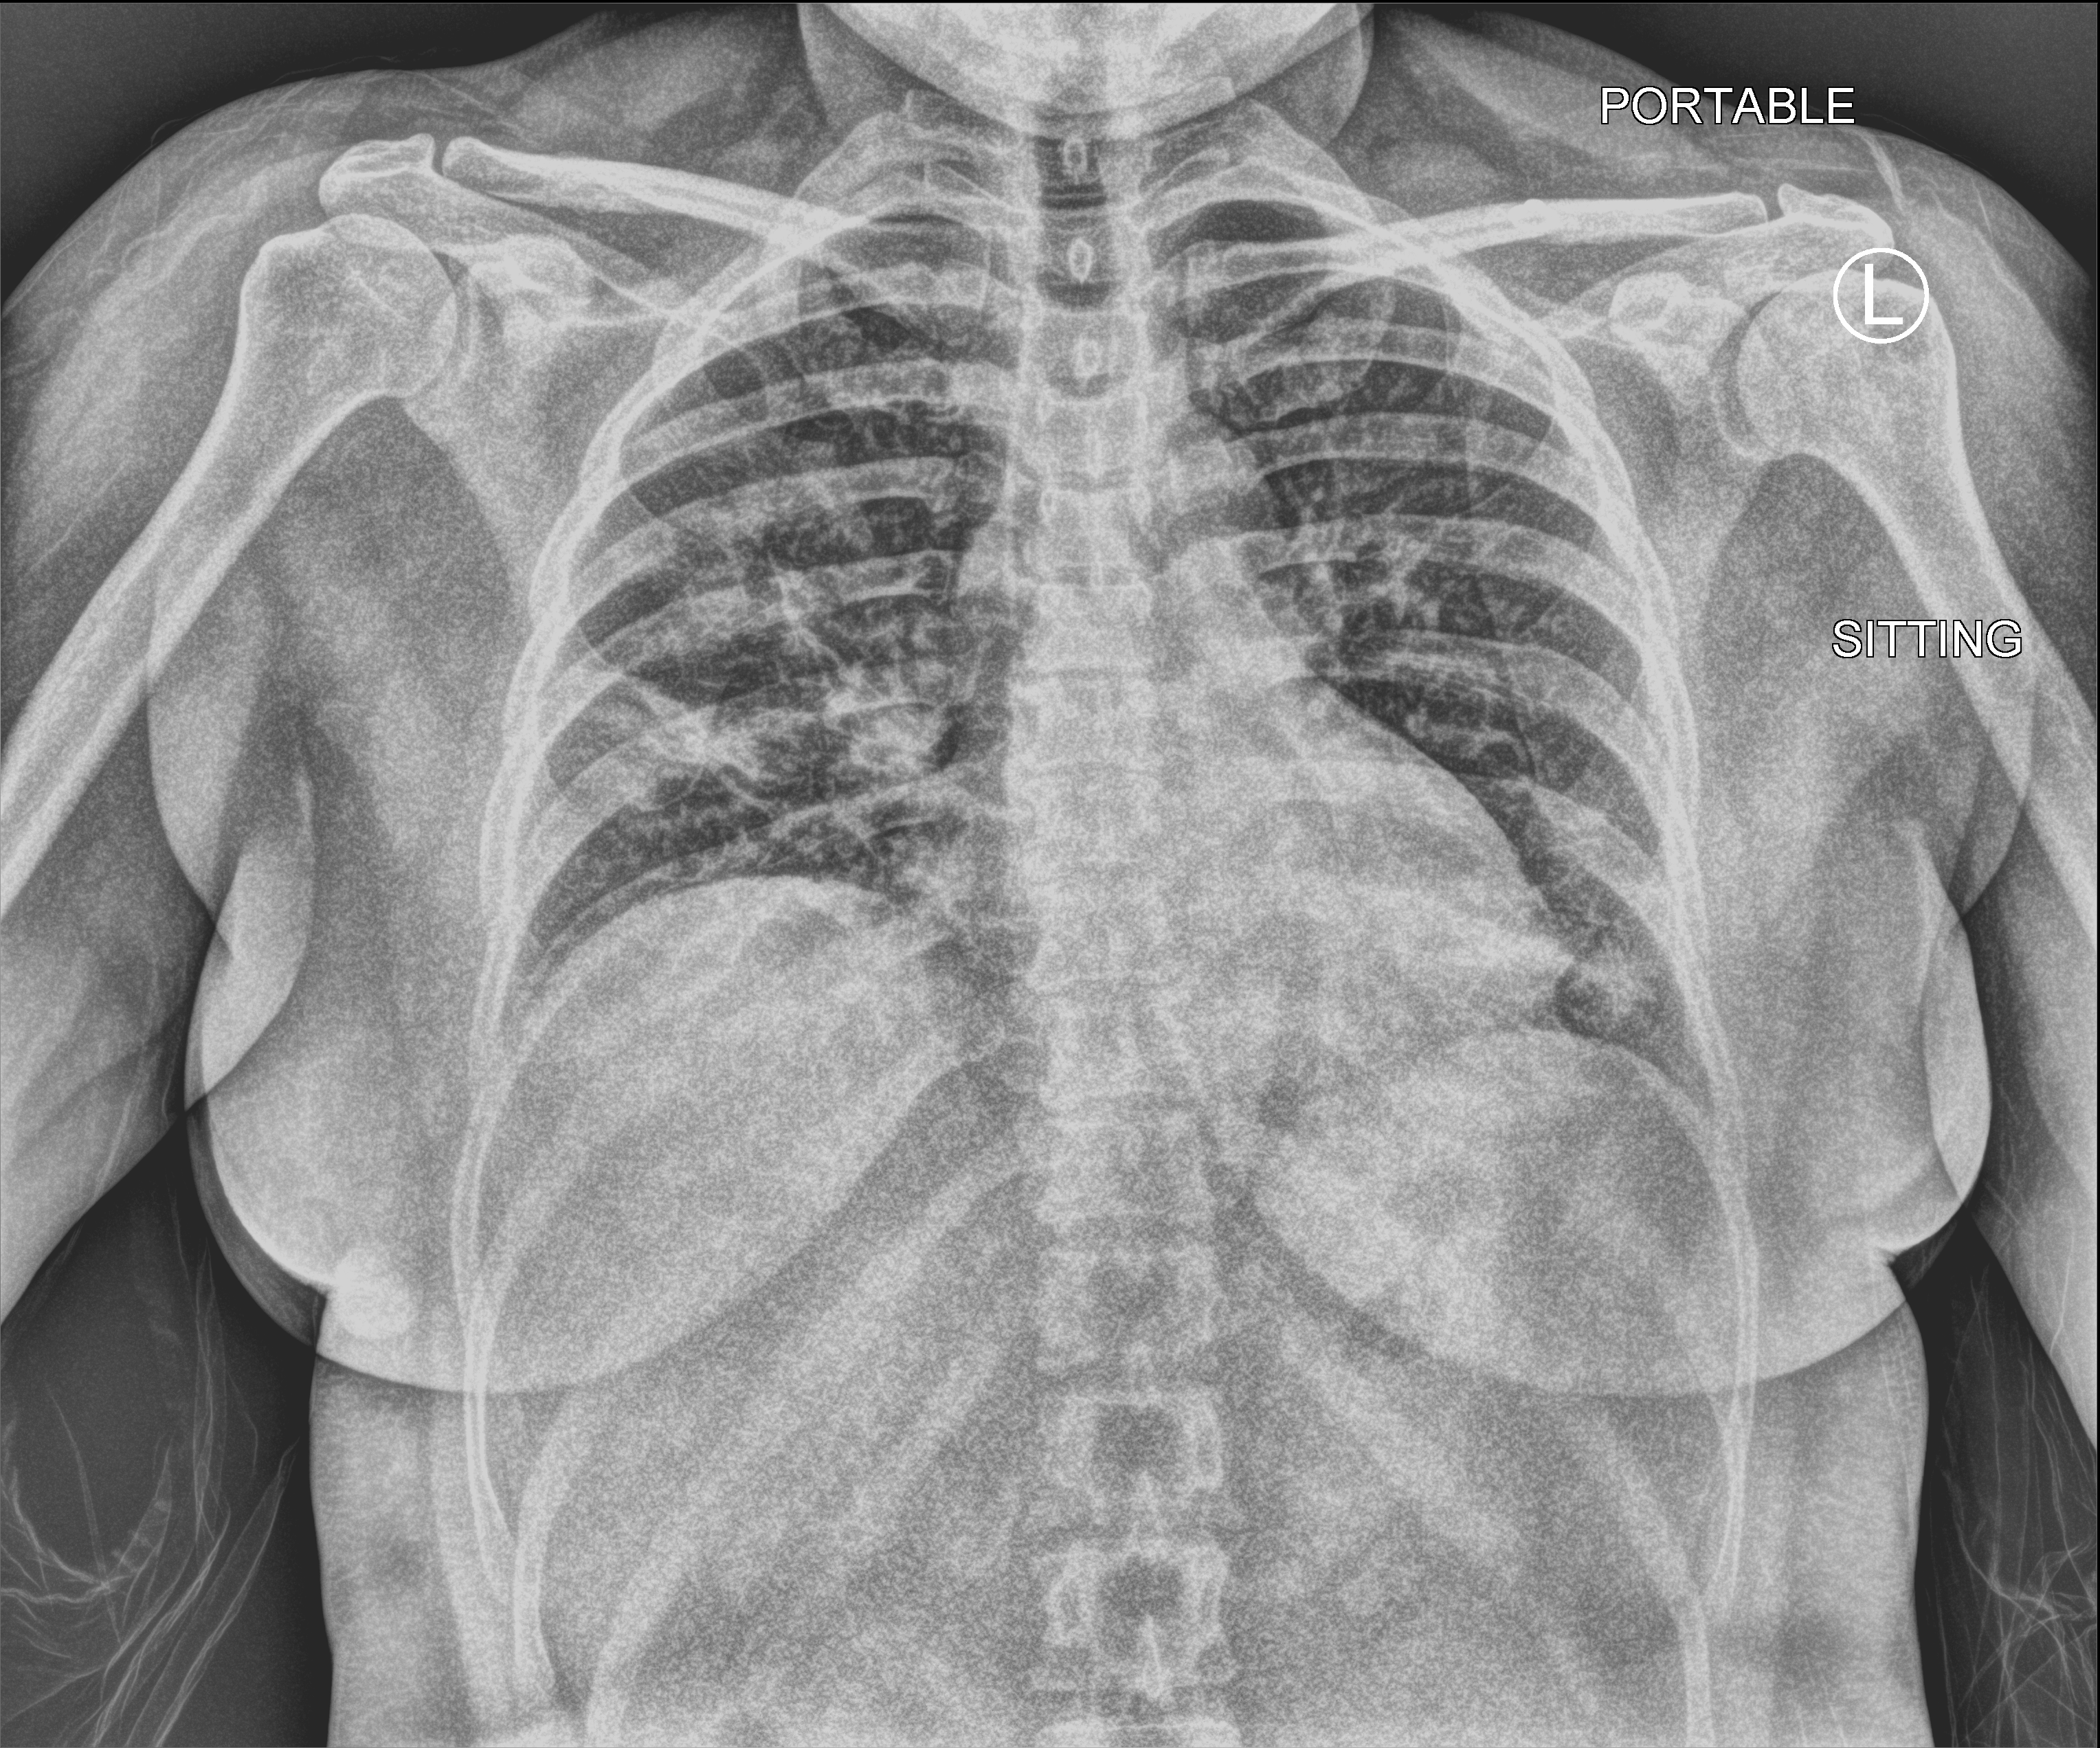
Chest X-ray (portable); anteroposterior (AP) projection. Female patient hospitalised with COVID-19, age 18–59 years.
From the hospital-stay record, not from the radiograph (when in the stay this image was taken is not recorded): admitted to intensive care during this hospital stay: no.